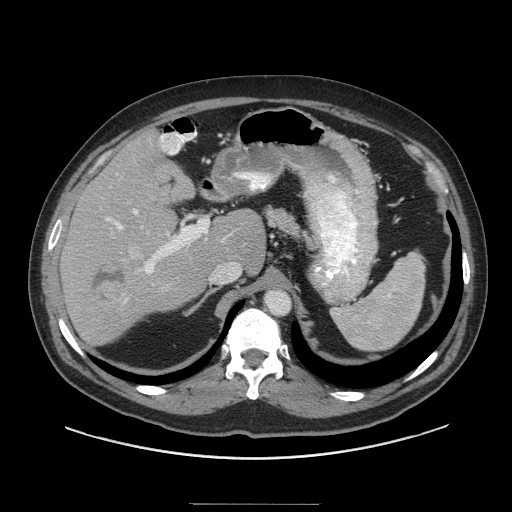
Contrast-enhanced abdominal CT (liver protocol), one axial slice. Position 63 of 91 along the scan axis. Soft-tissue window (W 400 / L 40 HU). 2.5 mm slice thickness. 512 × 512 image matrix. Case-level facts recorded for this patient, not image findings: diagnosis: hepatocellular carcinoma (patient treated with transarterial chemoembolisation; whether this scan precedes or follows treatment is not stated here); TNM stage (as recorded): Stage-I; Child-Pugh class: A; tumour differentiation: well differentiated; tumour size: 4 cm.
Annotated regions visible in this slice (semi-automatically segmented with operator editing):
- liver parenchyma outside the tumour (the mass and vessels are separate outlines, so this box may not span the whole liver): bounding box [x1, y1, x2, y2] px = [60, 134, 266, 346]
- mass: [89, 261, 128, 308]
- liver vessels: [106, 209, 241, 303]